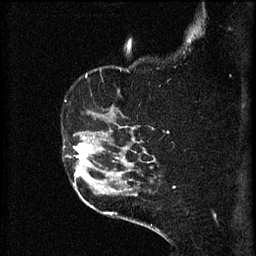
Breast MRI (dynamic contrast-enhanced), one sagittal slice; 3 images stored at this slice position (order not interpretable as contrast timing); 1.5 T; TE 4.2 ms, TR 8.2 ms; 2 mm slice thickness; 256 × 256 image matrix, field of view 180 × 180 mm. Female patient, age 49 years.
Outlined on this slice (semi-automatic segmentation, software-assisted and operator-edited):
- analysis volume of interest (the breast-tissue region the enhancement analysis was run in; not a lesion): bounding box <64,132,105,177> (left, top, right, bottom; pixels)
- tumour enhancement mask (voxels above the 70 % enhancement threshold inside the analysis volume of interest): <73,136,103,177>